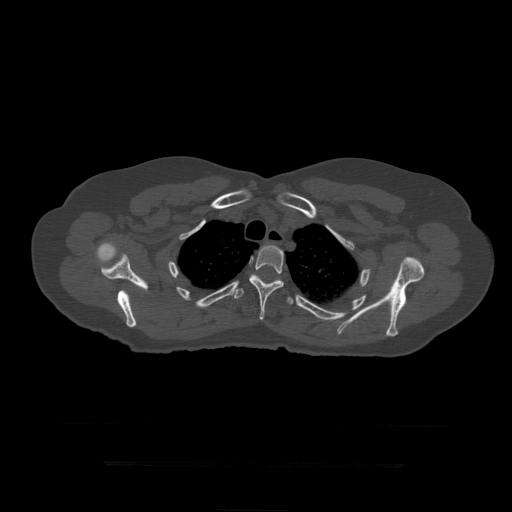
CT including the spine, one axial slice. Position 348 of 399 along the scan axis. Reconstruction kernel STANDARD. 120 kVp. Bone window (W 1800 / L 400 HU). 1.25 mm slice thickness. 512 × 512 image matrix, field of view 450 × 450 mm. Patient age 41 years. From the clinical record (not read from this slice): primary cancer: breast.
Structures marked on this image (semi-automatic segmentation, software-assisted and operator-edited):
- T4 vertebra: bounding box (x1, y1, x2, y2) in pixels: (249, 244, 284, 320)
- T5 vertebra: (234, 275, 294, 305)